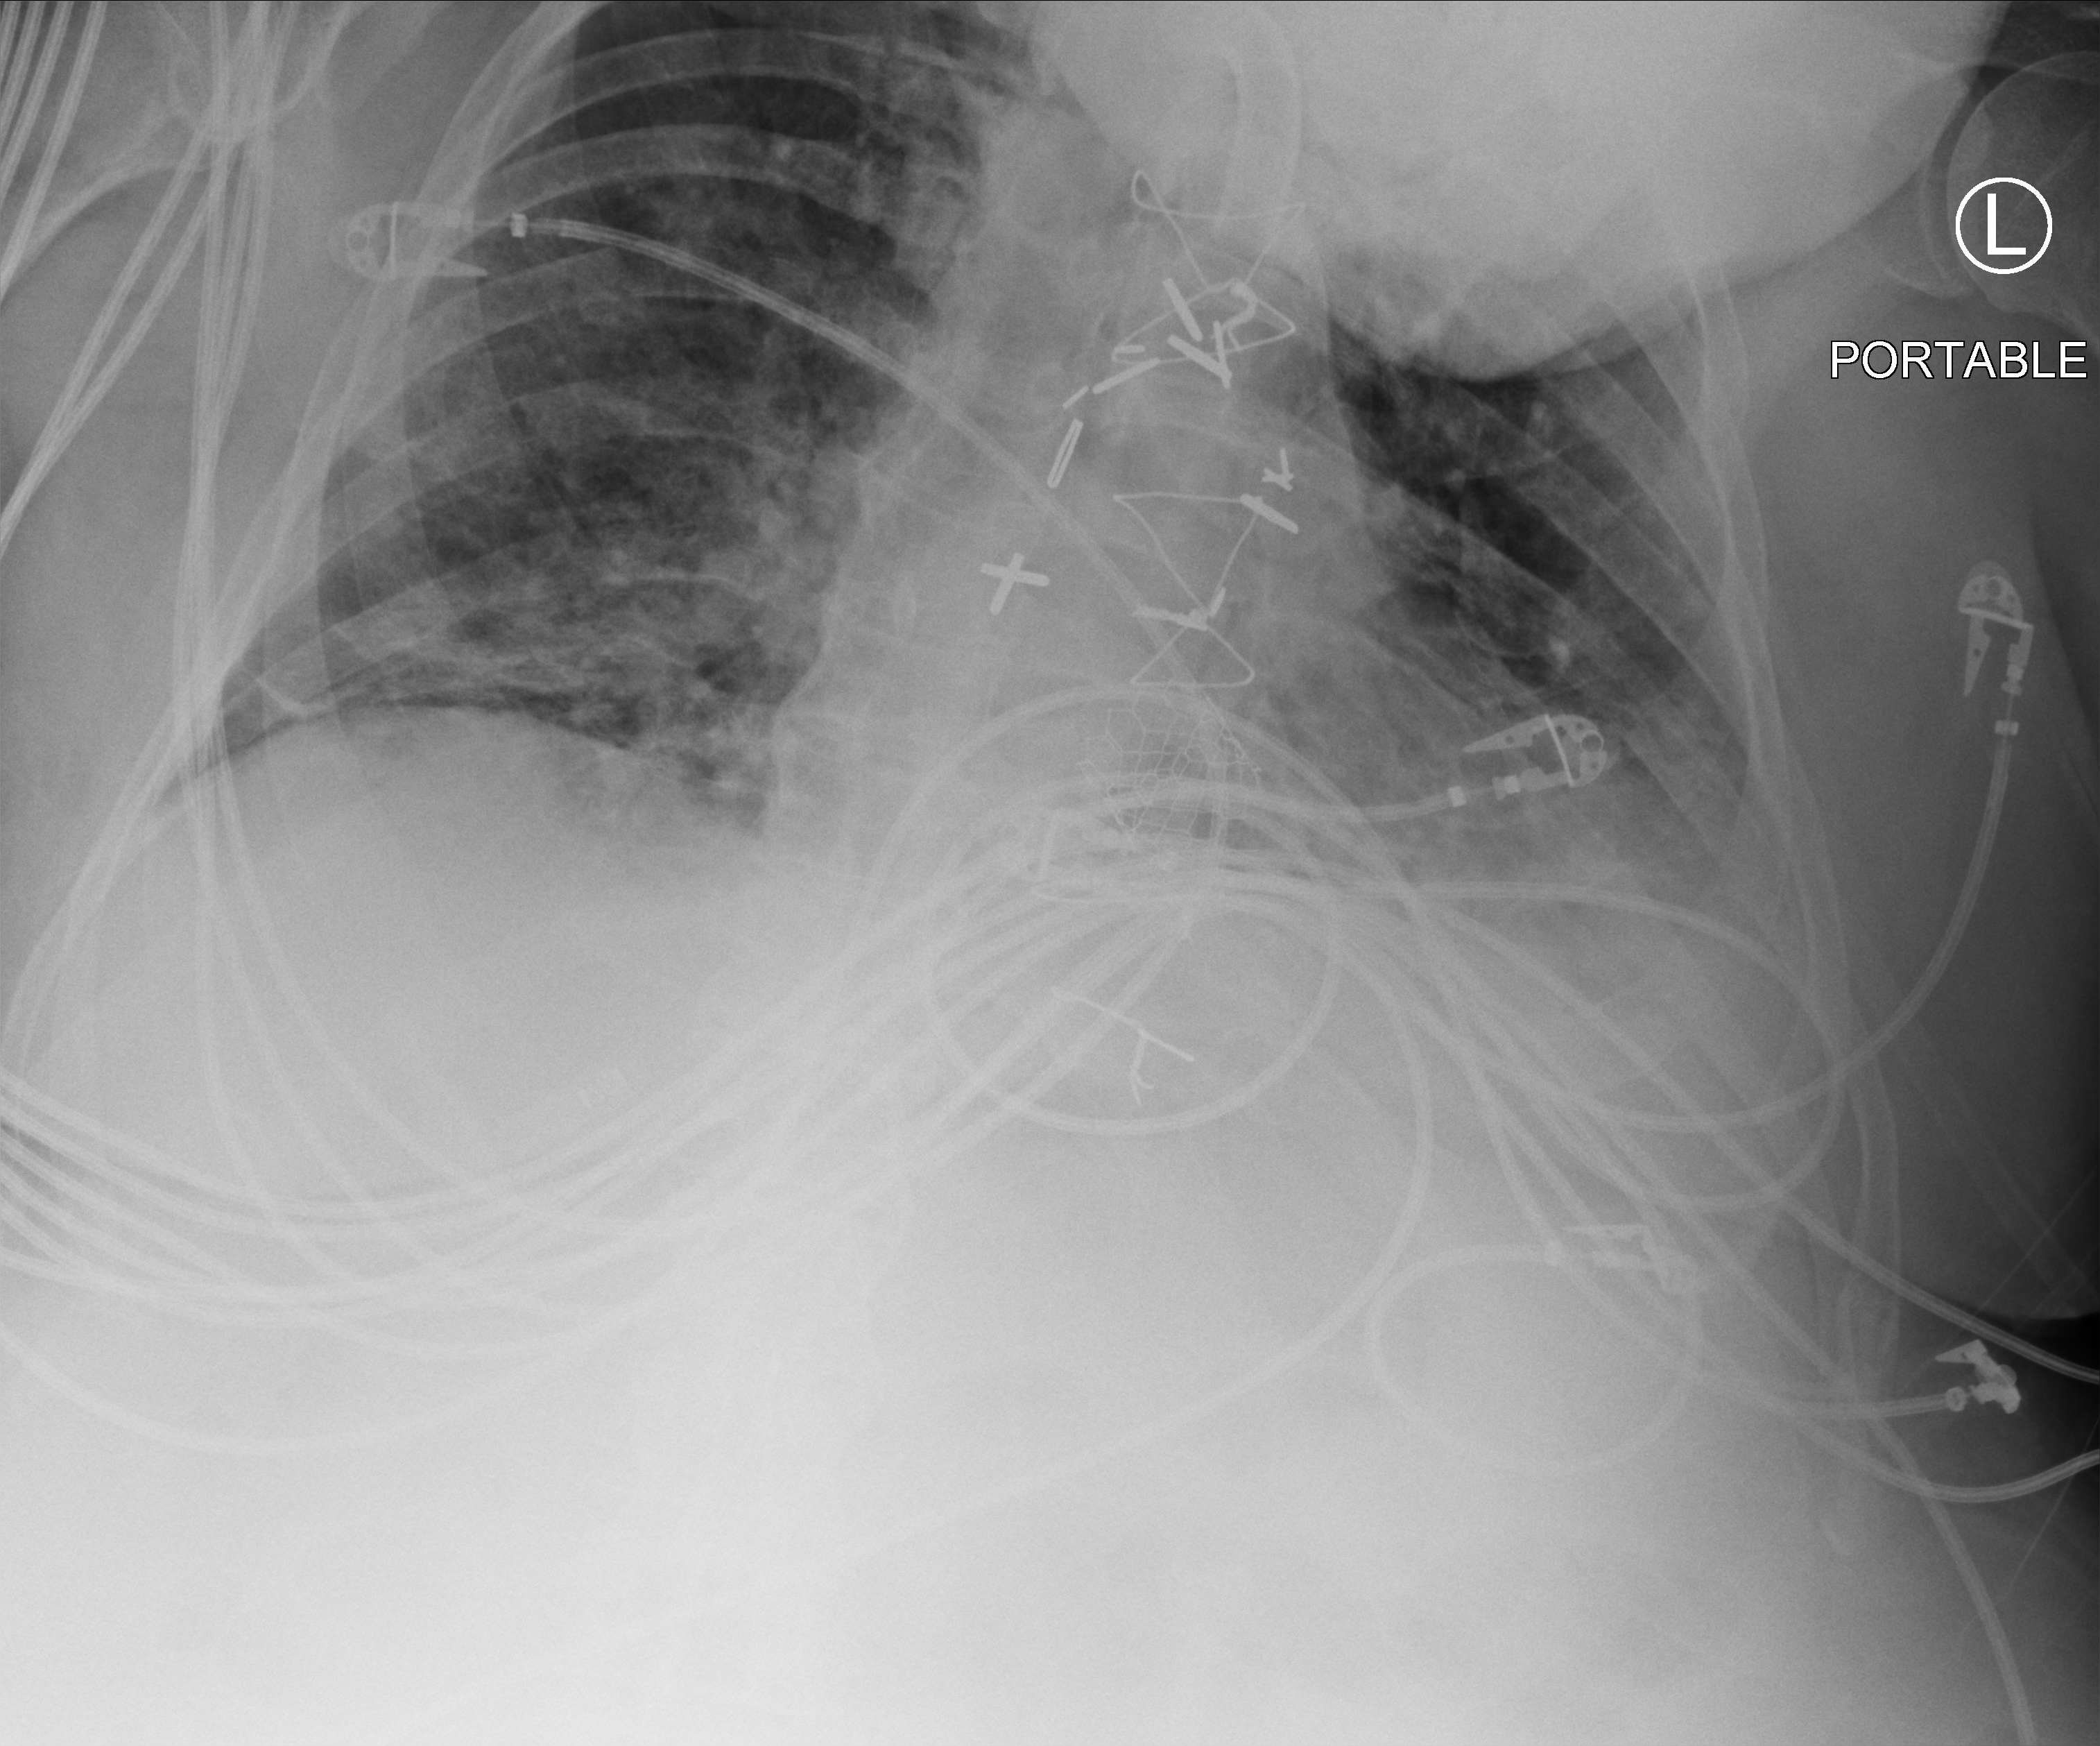
Bedside chest radiograph (computed radiography), anteroposterior (AP) projection. Patient hospitalised with COVID-19; male, aged 60–74 years.
Hospital-stay facts (about this admission, not read from this image; timing relative to this image not recorded): mechanically ventilated during this hospital stay: yes.